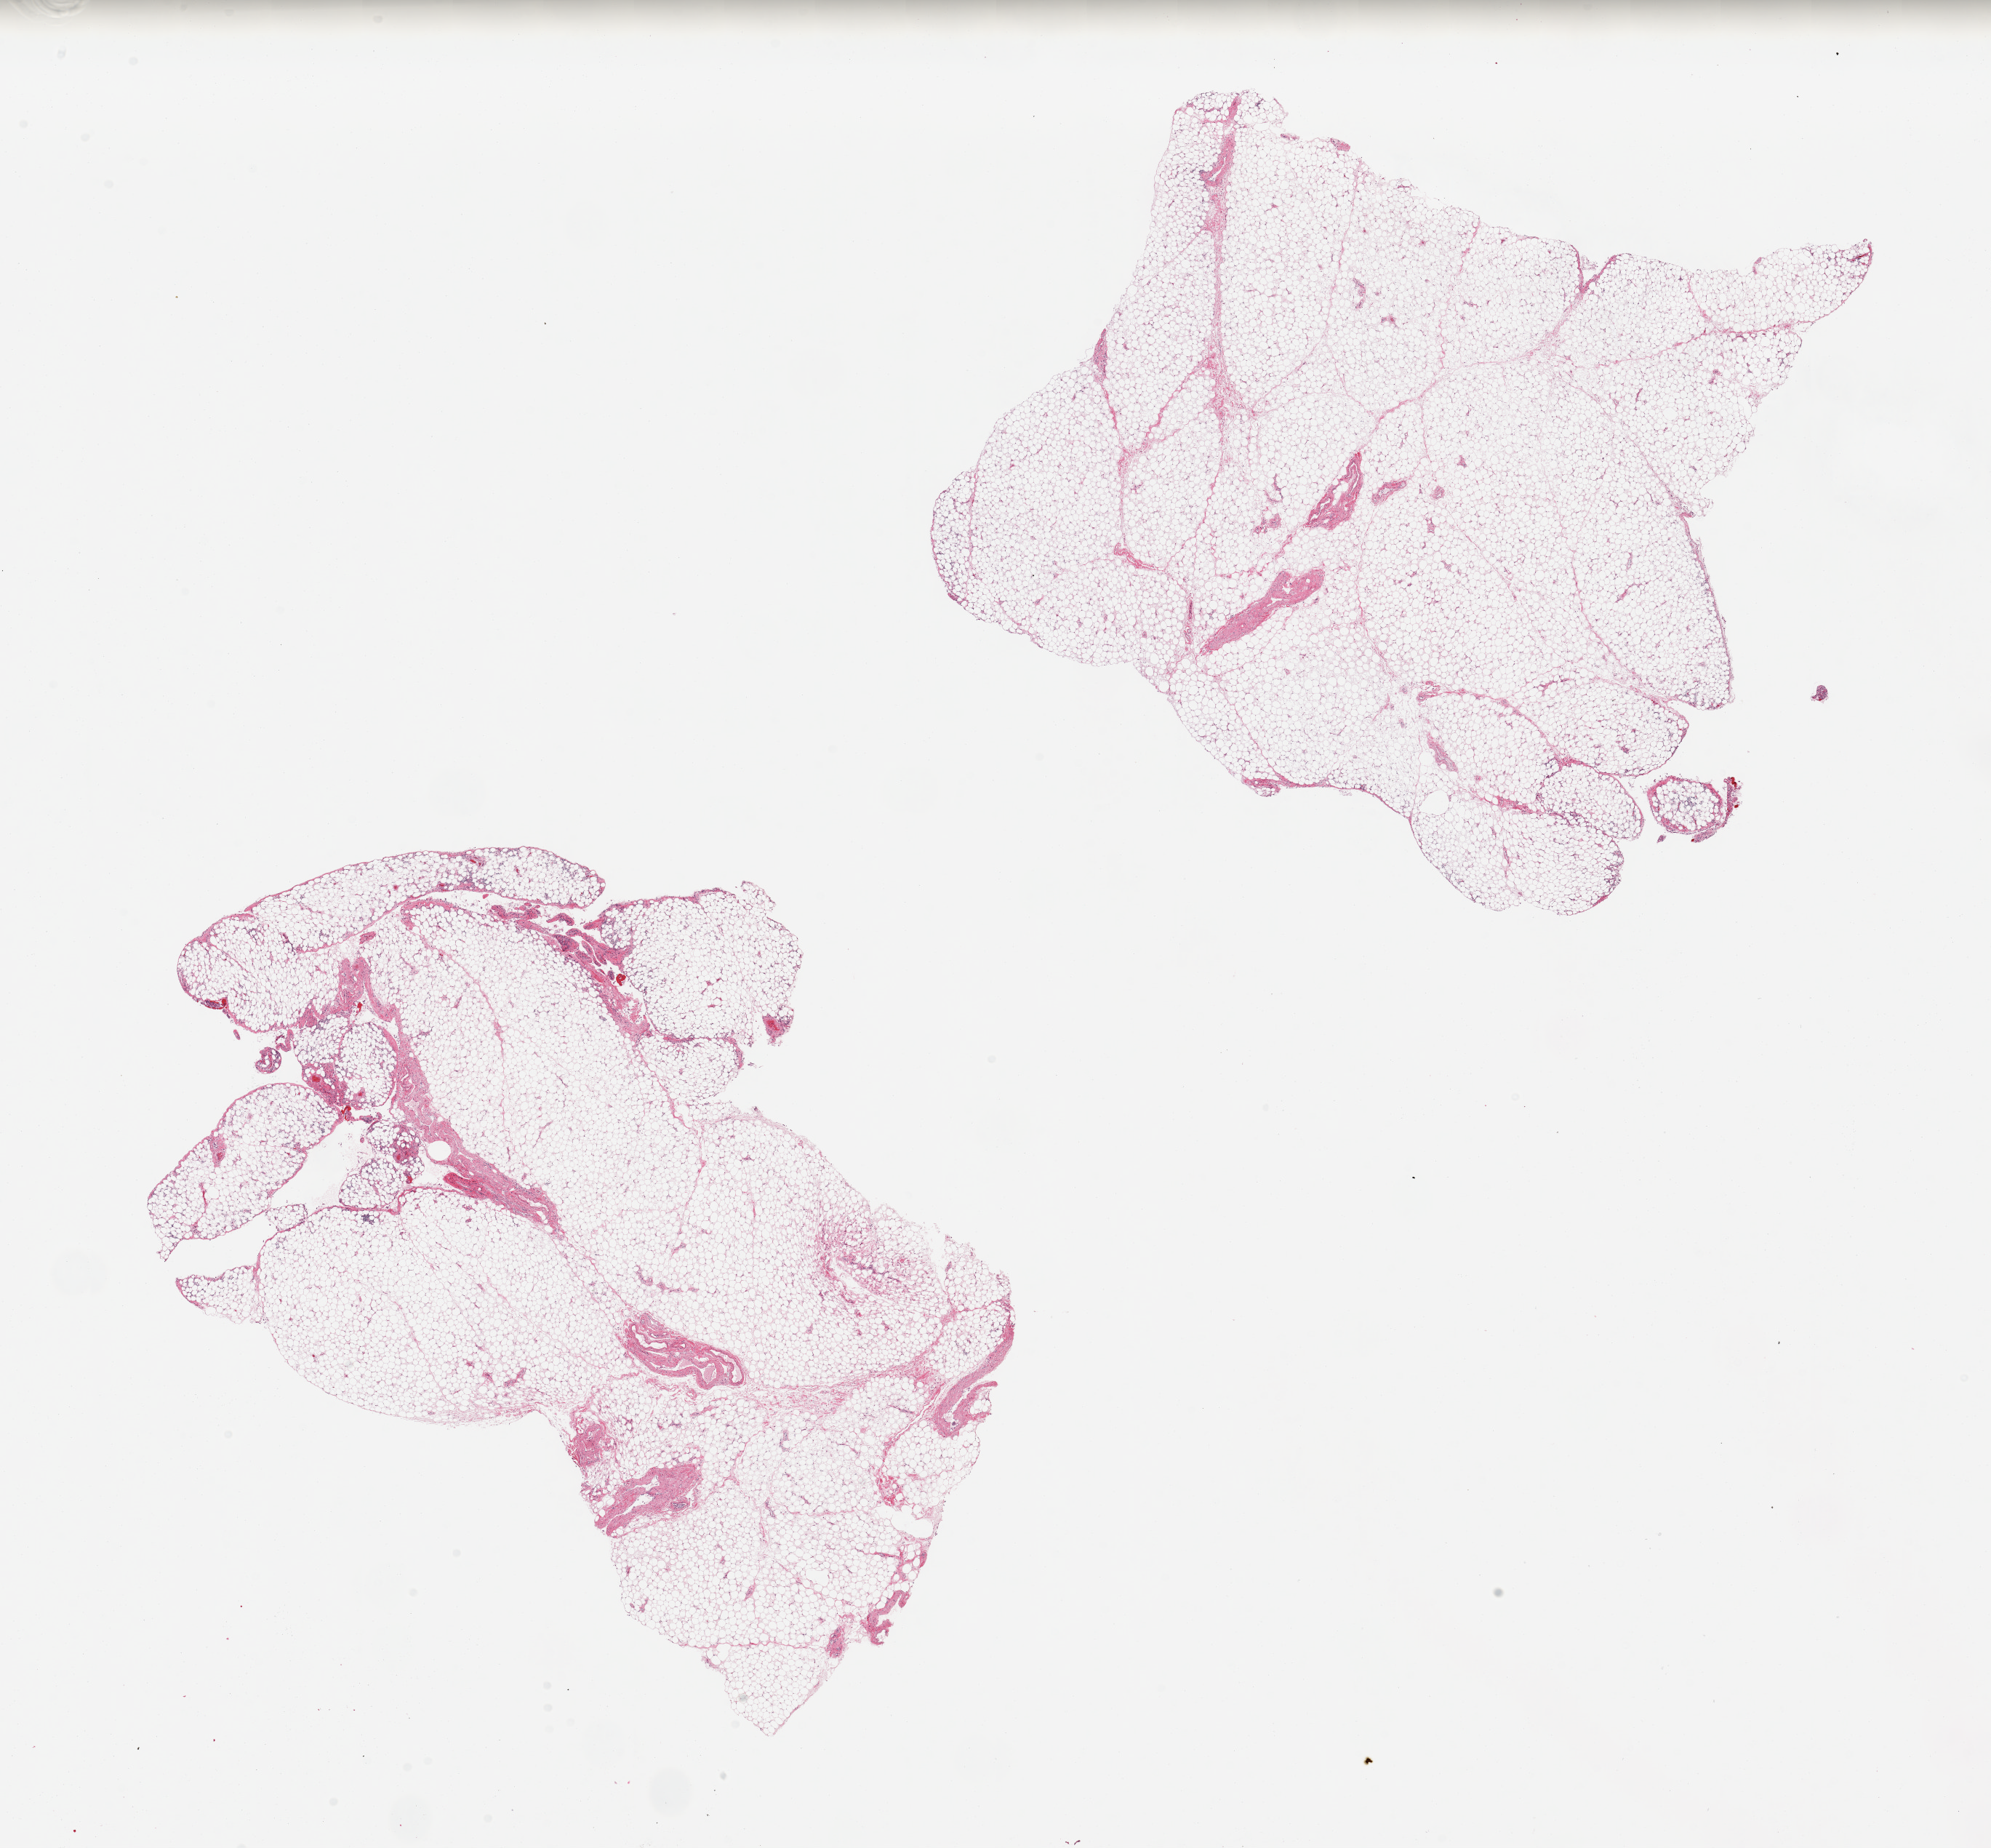
Hematoxylin and eosin (H&E) whole-slide image, brightfield, shown as a low-resolution overview of the whole scanned area (about 21.7 x 20.1 mm); PAXgene-fixed, paraffin-embedded tissue; target tissue: omentum; donor tissue sample. Donor: male.
- pathologist's review note for this sample: 2 pieces; mild scattered inflammatory cell infiltrate [history of ascites]